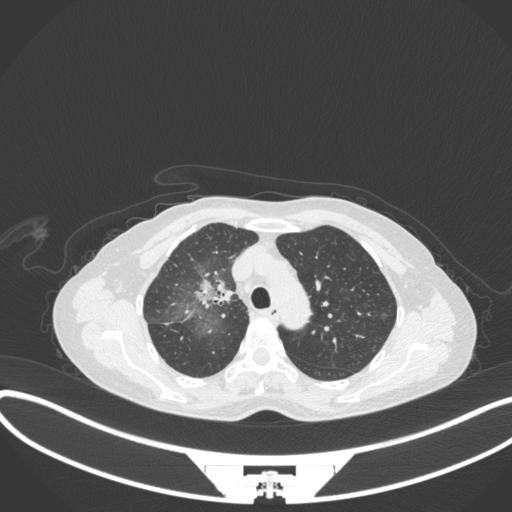
Chest CT, one axial slice. Slice 232 of 311 in the series (ordered by position). Reconstruction kernel B31f. 120 kVp. Lung window (W 1500 / L -600 HU). 1 mm slice thickness. 512 × 512 image matrix, field of view 400 × 400 mm. Patient: female, 59 years. From the clinical record (not read from this slice): clinical TNM (as recorded): T3 N0 M0; histopathological grade: G1.
Structures marked on this image (rectangle marked by the reading radiologist):
- lung tumour (recorded histology: adenocarcinoma): bounding box <192,272,235,314> (left, top, right, bottom; pixels)